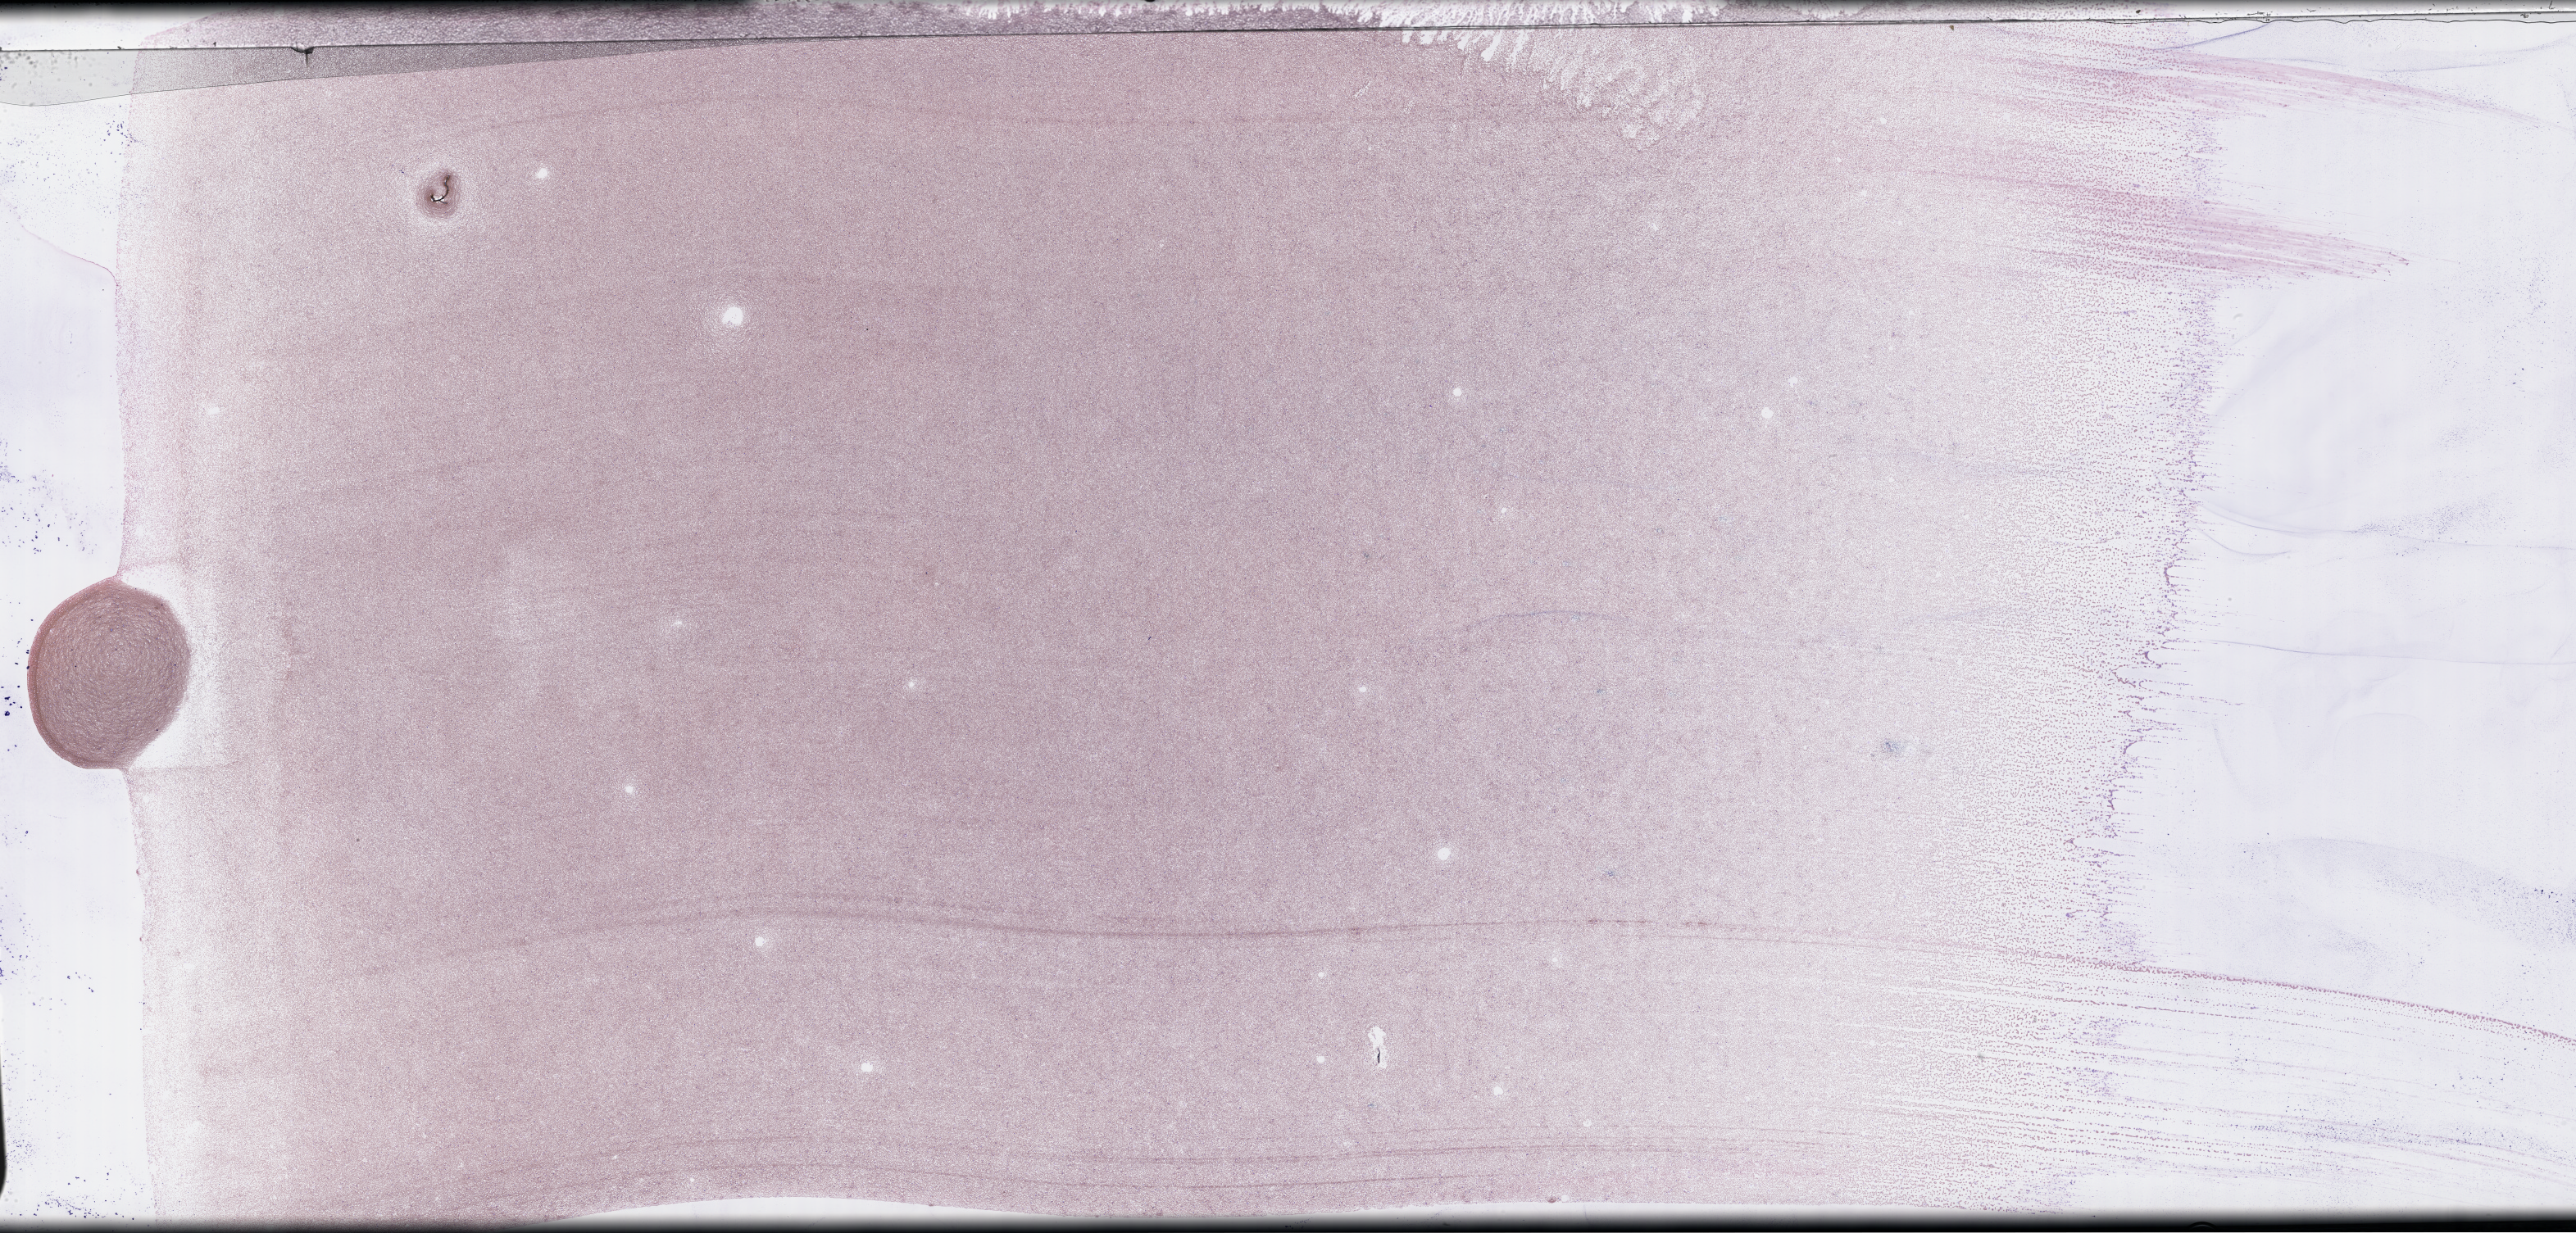
Whole-slide image of a bone marrow smear, Wright–Giemsa stain — low-resolution overview of the scanned area, about 50.8 x 24.3 mm; collected at baseline (before treatment). Male patient.
Patient diagnosis: Plasma Cell Myeloma.